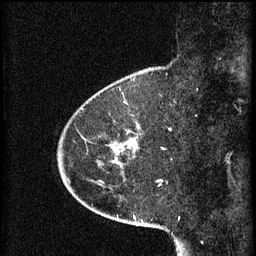
Breast MRI (dynamic contrast-enhanced), one sagittal slice. Slice 15 of 60 in the series (ordered by position). 3 images stored at this slice position (order not interpretable as contrast timing). 1.5 T. TE 4.2 ms, TR 8.2 ms. 2 mm slice thickness. 256 × 256 image matrix, field of view 200 × 200 mm. Patient: female, 45 years.
Structures marked on this image (semi-automatically segmented with operator editing):
- analysis volume of interest (the breast-tissue region the enhancement analysis was run in; not a lesion): box from (x=80, y=102) to (x=141, y=167) px
- tumour enhancement mask (voxels above the 70 % enhancement threshold inside the analysis volume of interest): (x=112, y=140)–(x=136, y=149)